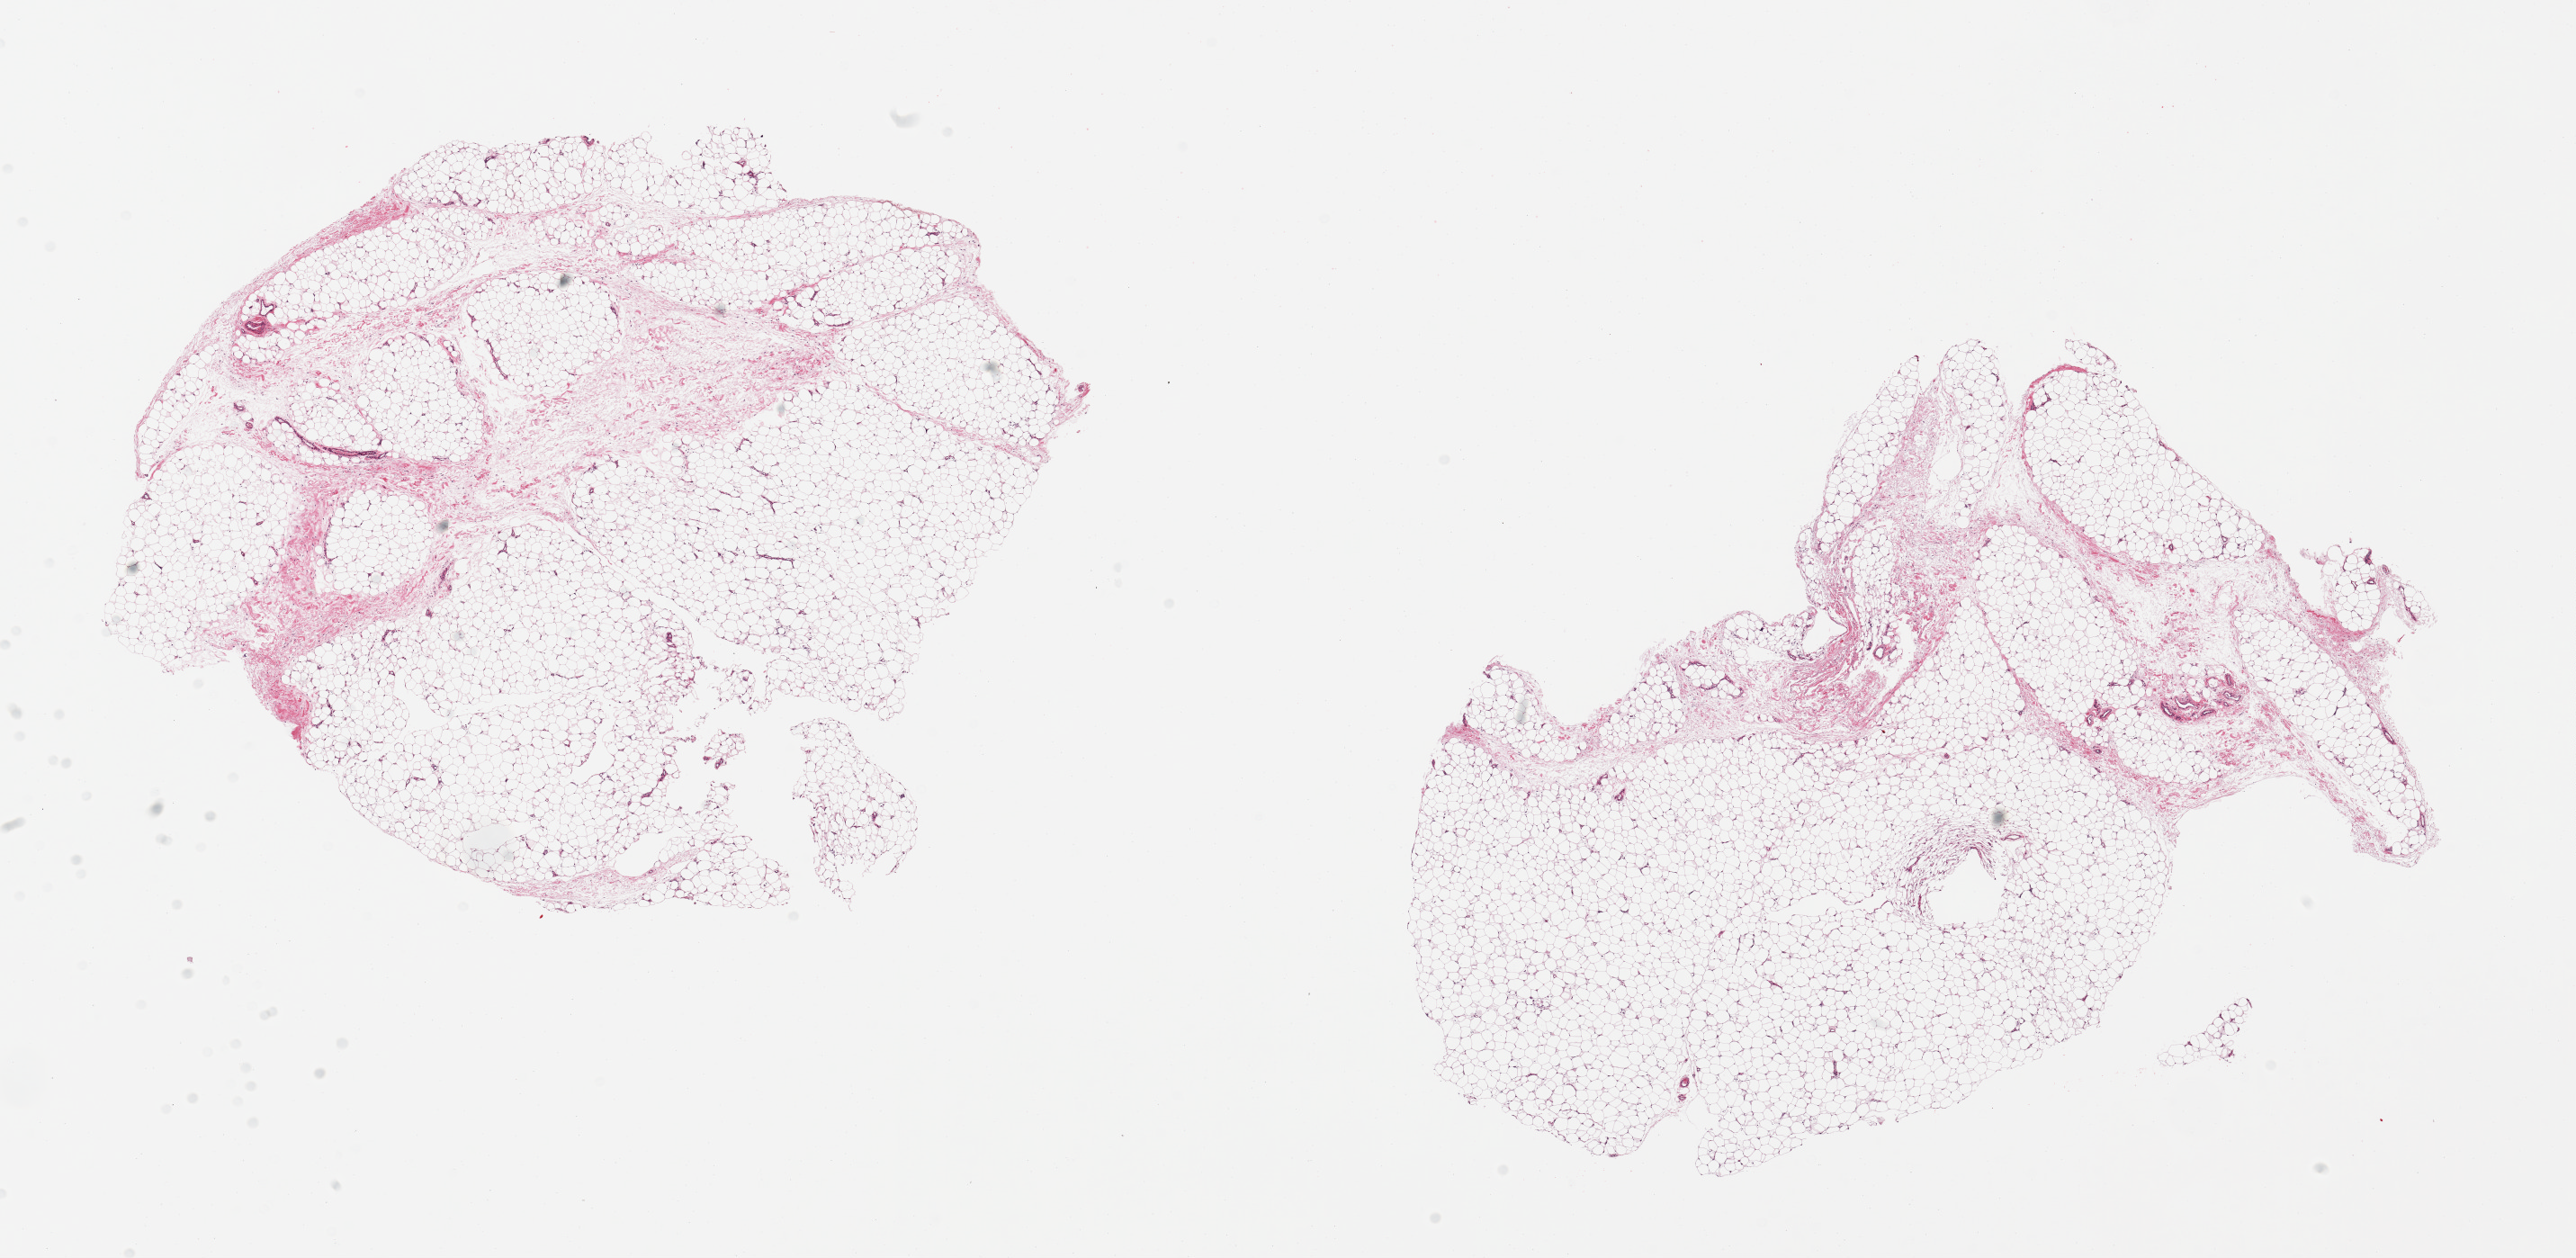
Whole-slide image, H&E stain — shown as a low-resolution overview of the whole scanned area (about 22.6 x 11.1 mm, acquisition: 20x scan), PAXgene-fixed, paraffin-embedded tissue, sampled site (target tissue): adipose tissue, tissue donor sample. Donor sex: female.
Pathologist's review note for this sample: 2 pieces, <10% fascia/vascular elements.